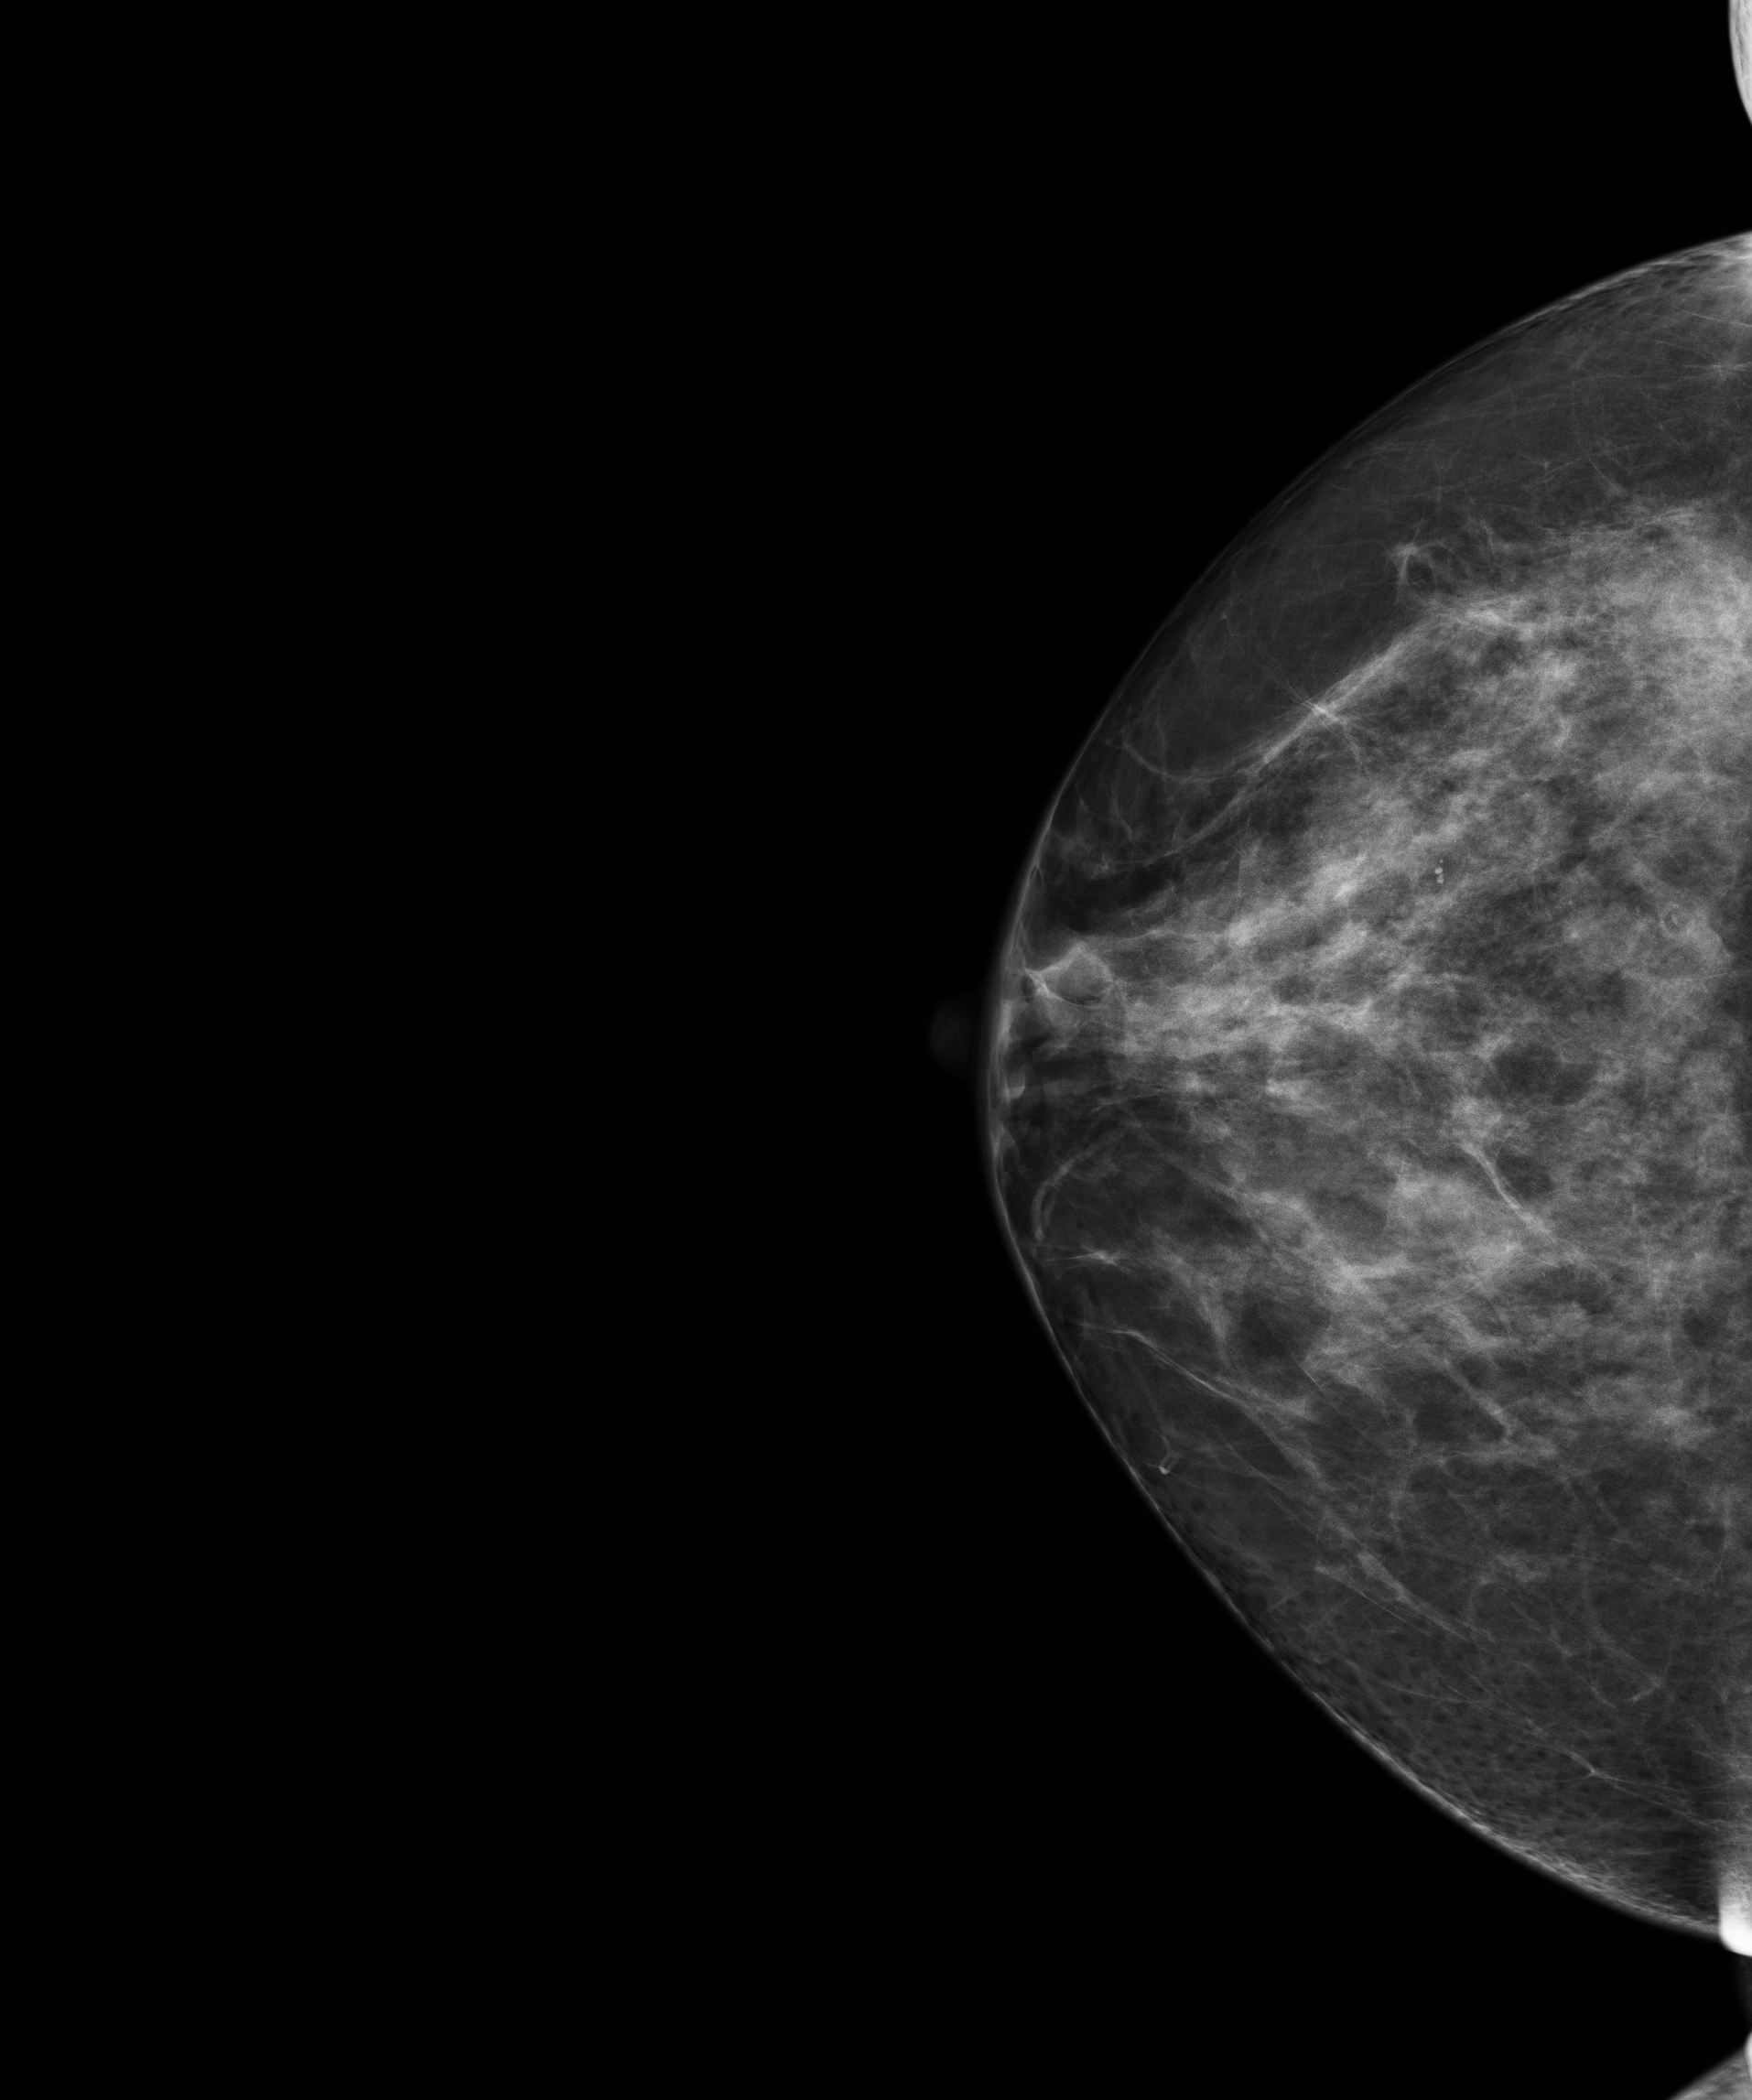
Screening examination; compressed breast thickness 62 mm; system: Senographe Essential ADS_56.21.3. Female patient, age 45 years.
Image type: full-field digital mammogram. Breast: right. Projection: CC view. BI-RADS breast density category at the screening exam (both breasts, scale 1–4): 3. Final BI-RADS assessment for this screening round (tomosynthesis exam, both breasts): category 1. Recall: no recall after this screen.